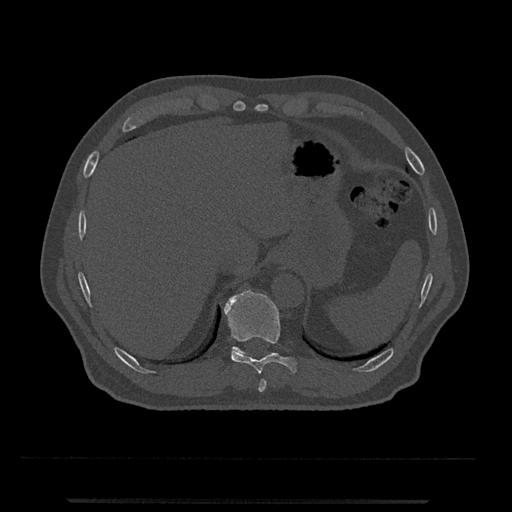
CT including the spine, one axial slice. Position 511 of 797 along the scan axis. Reconstruction kernel Br40s/3. 120 kVp. Bone window (W 1800 / L 400 HU). 0.5 mm slice thickness. 512 × 512 image matrix. Male patient, age 63 years. Case-level facts recorded for this patient, not image findings: primary cancer: prostate.
Structures marked on this image (semi-automatic segmentation, software-assisted and operator-edited):
- T10 vertebra: box from (x=223, y=289) to (x=298, y=374) px
- T11 vertebra: (x=231, y=346)–(x=272, y=356)
- T9 vertebra: (x=258, y=379)–(x=267, y=392)